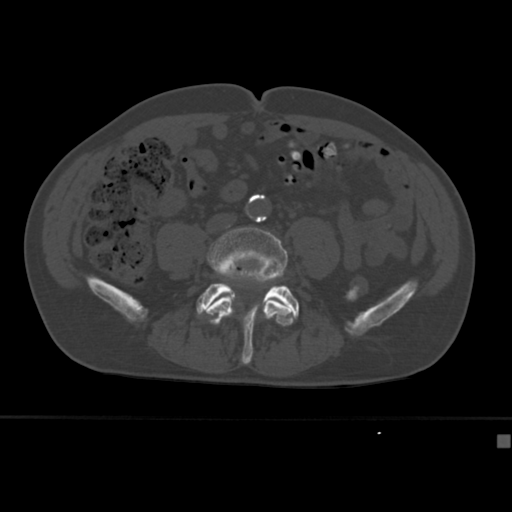
CT including the spine, one axial slice; position 97 of 430 along the scan axis; reconstruction kernel Br40s; bone window (W 1800 / L 400 HU); 512 × 512 image matrix. Patient: male, 64 years. Case-level facts recorded for this patient, not image findings: primary cancer: uterus; vertebrae with lytic lesions (as recorded): T1, T4, T5, T7, L5.
Annotated regions visible in this slice (semi-automatically segmented with operator editing):
- L4 vertebra: box from (x=204, y=227) to (x=293, y=326) px
- L5 vertebra: (x=196, y=283)–(x=299, y=364)